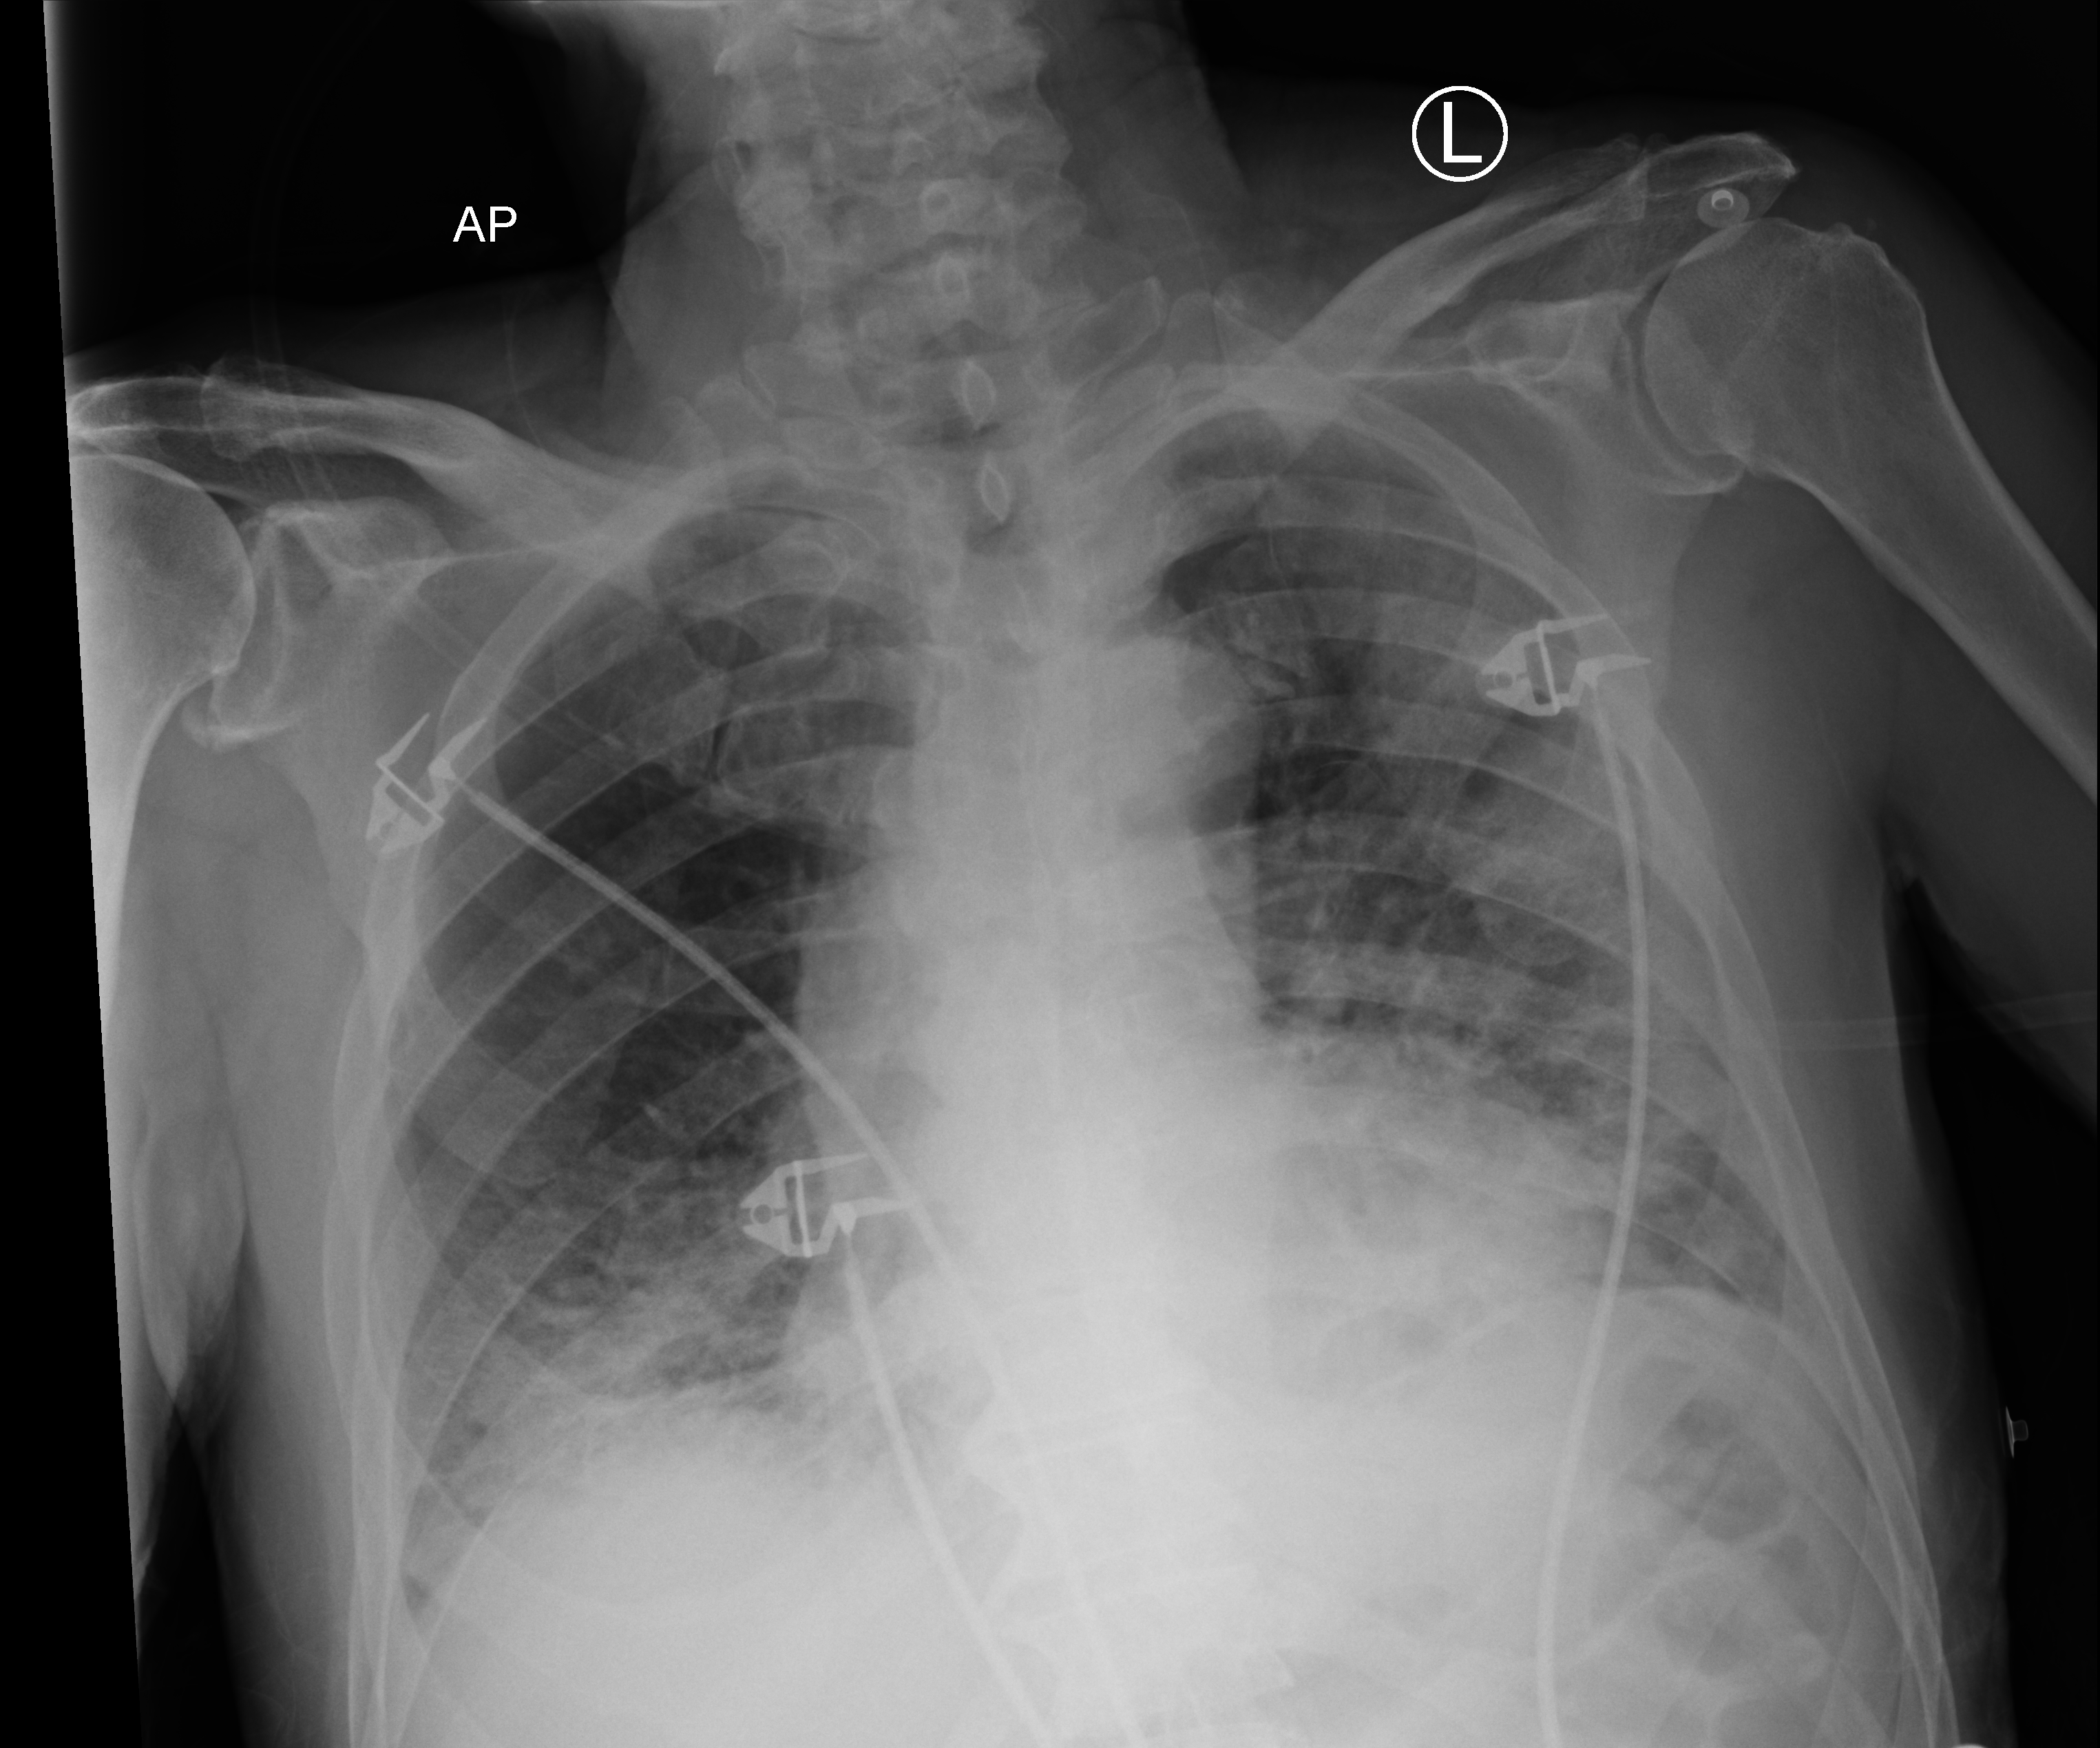
Portable chest radiograph, anteroposterior (AP) projection. Patient hospitalised with COVID-19; male, aged 75–90 years.
Hospital-stay facts (about this admission, not read from this image; timing relative to this image not recorded):
- admitted to intensive care during this hospital stay: yes